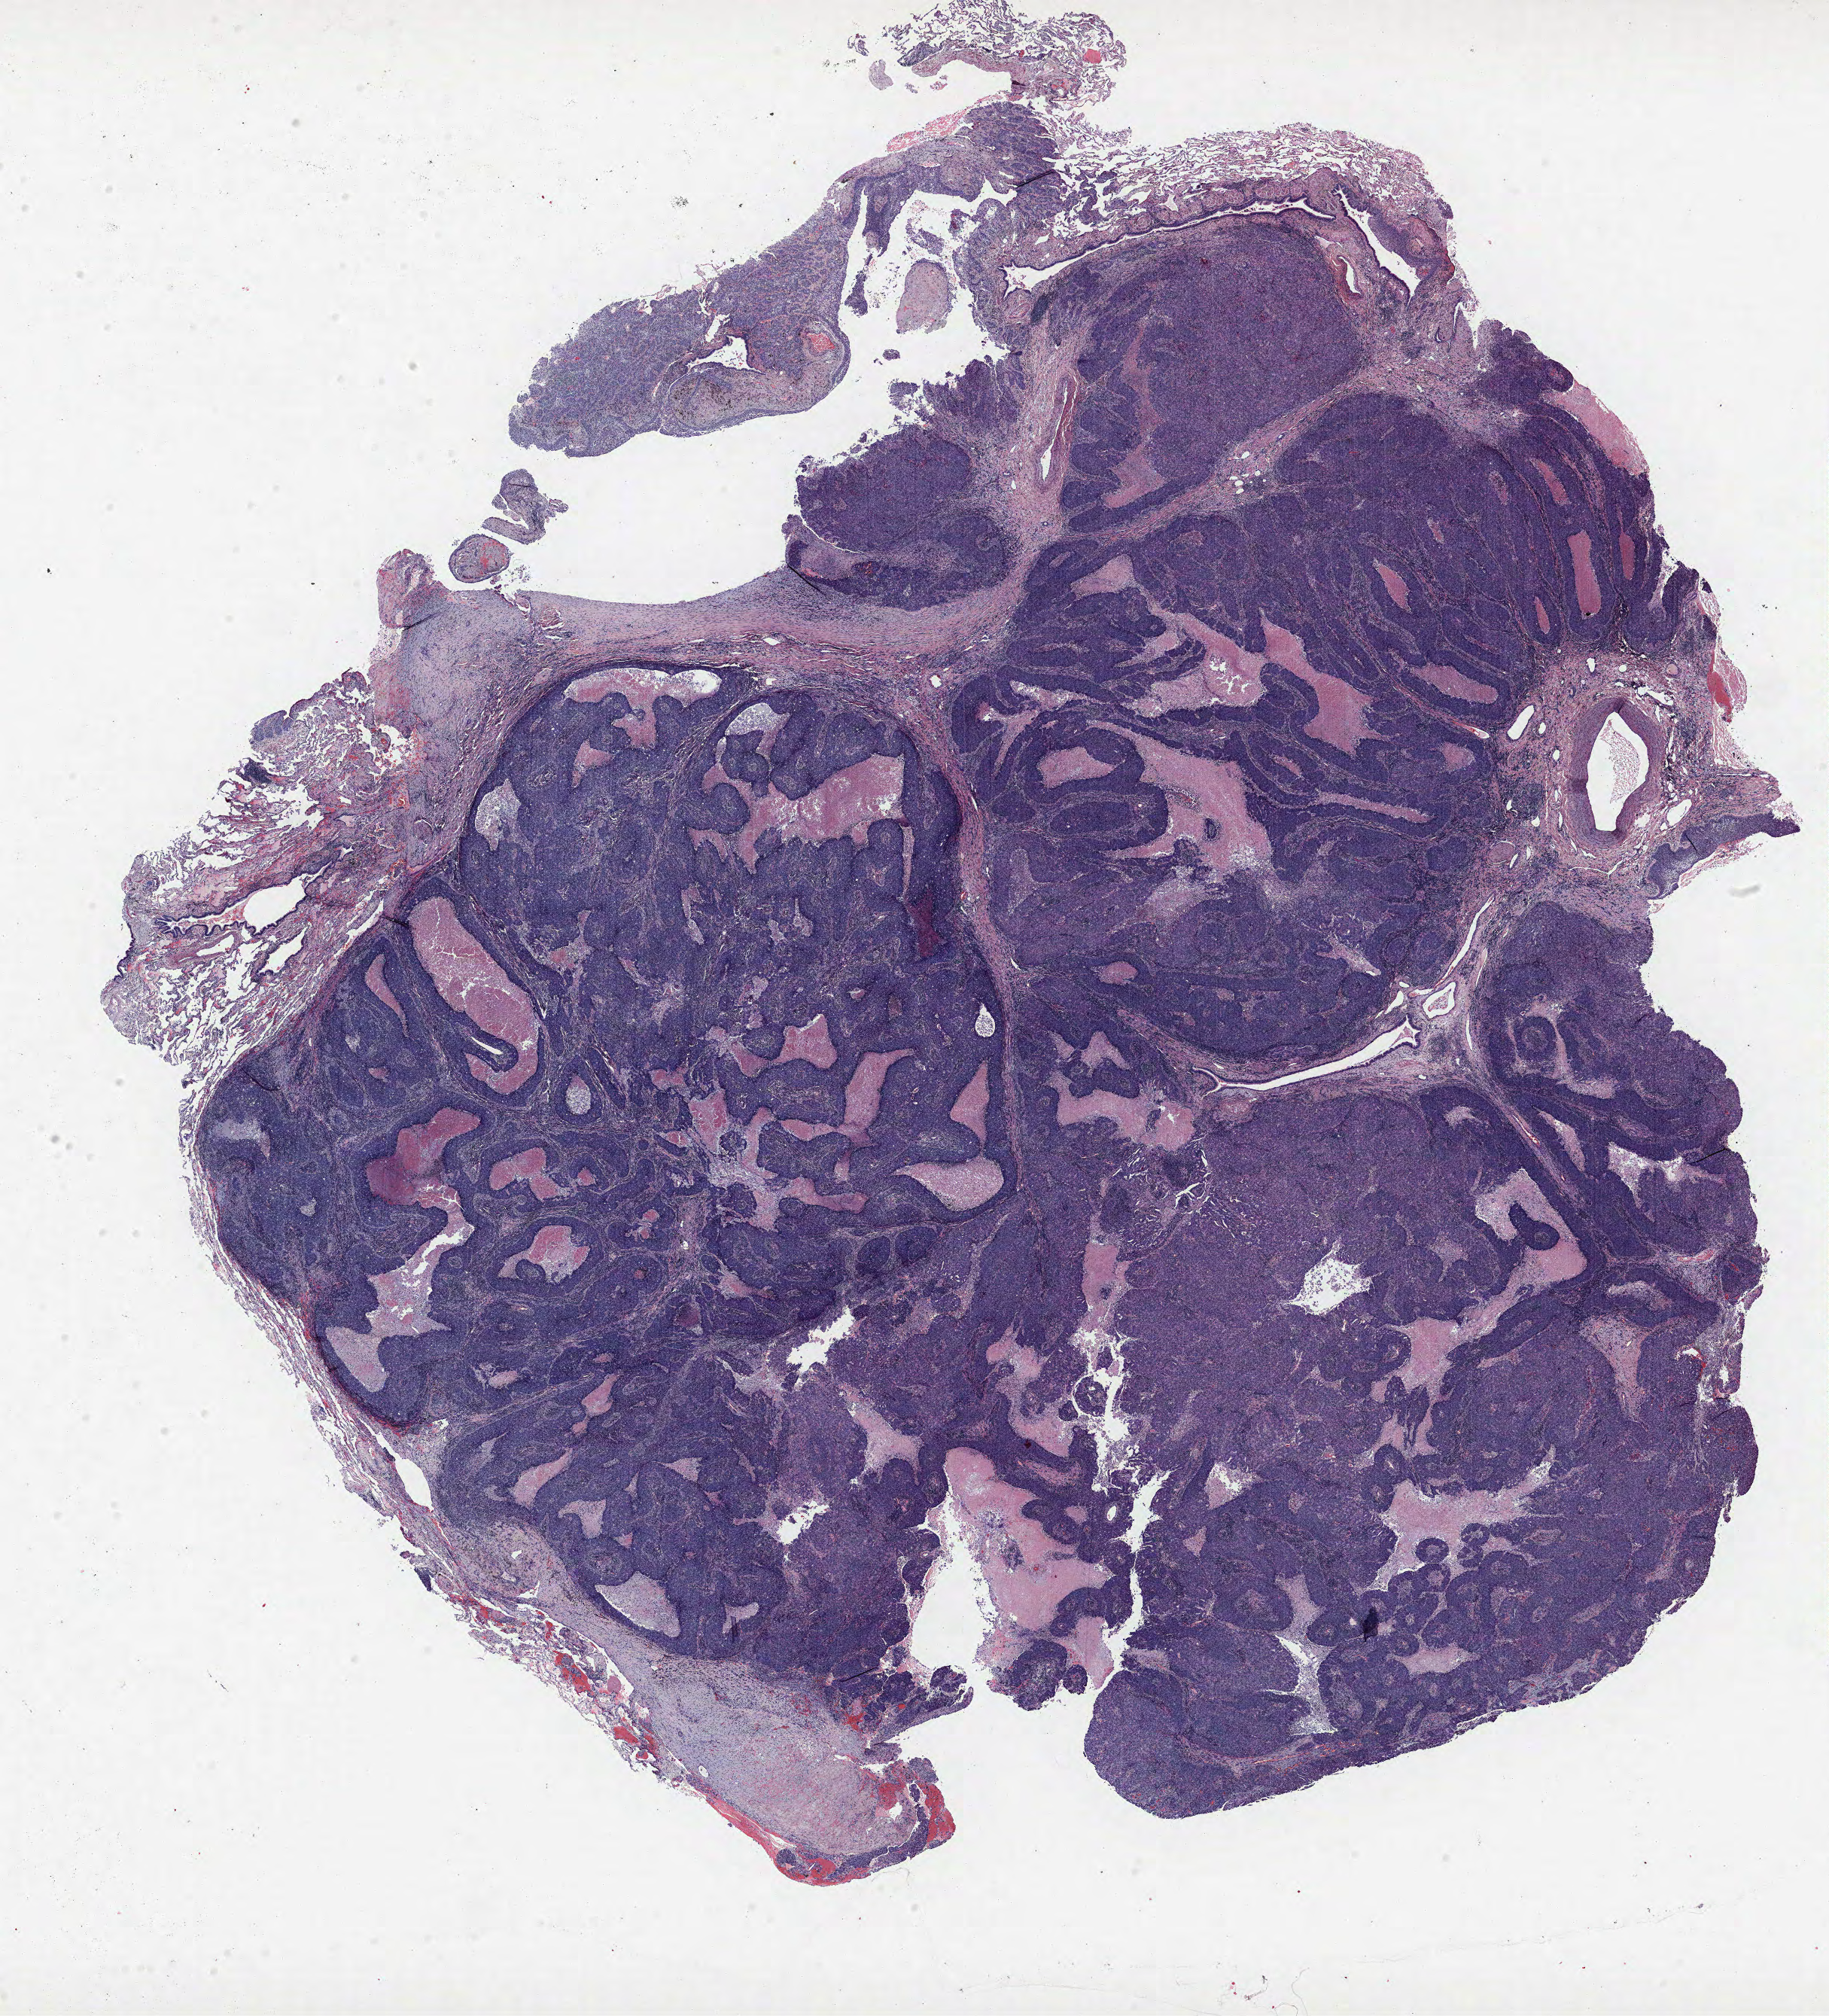
Whole-slide histology image, Hematoxylin and eosin (H&E) stained — whole scanned area (about 19.4 x 21.4 mm, acquisition: 40x scan) shown as a low-resolution overview; formalin-fixed paraffin-embedded (FFPE) section; lung. Female, age 69 at enrolment. Former smoker at enrolment. Grade: poorly differentiated (G3).
* primary tumour location (clinical record): right lower lobe
* ICD-O-3 topography: lower lobe of lung (C34.3)
* stage (AJCC 6th edition): IB
* tumour size (pathology): 36 mm
* participant's lung-cancer diagnosis: Non-small cell carcinoma